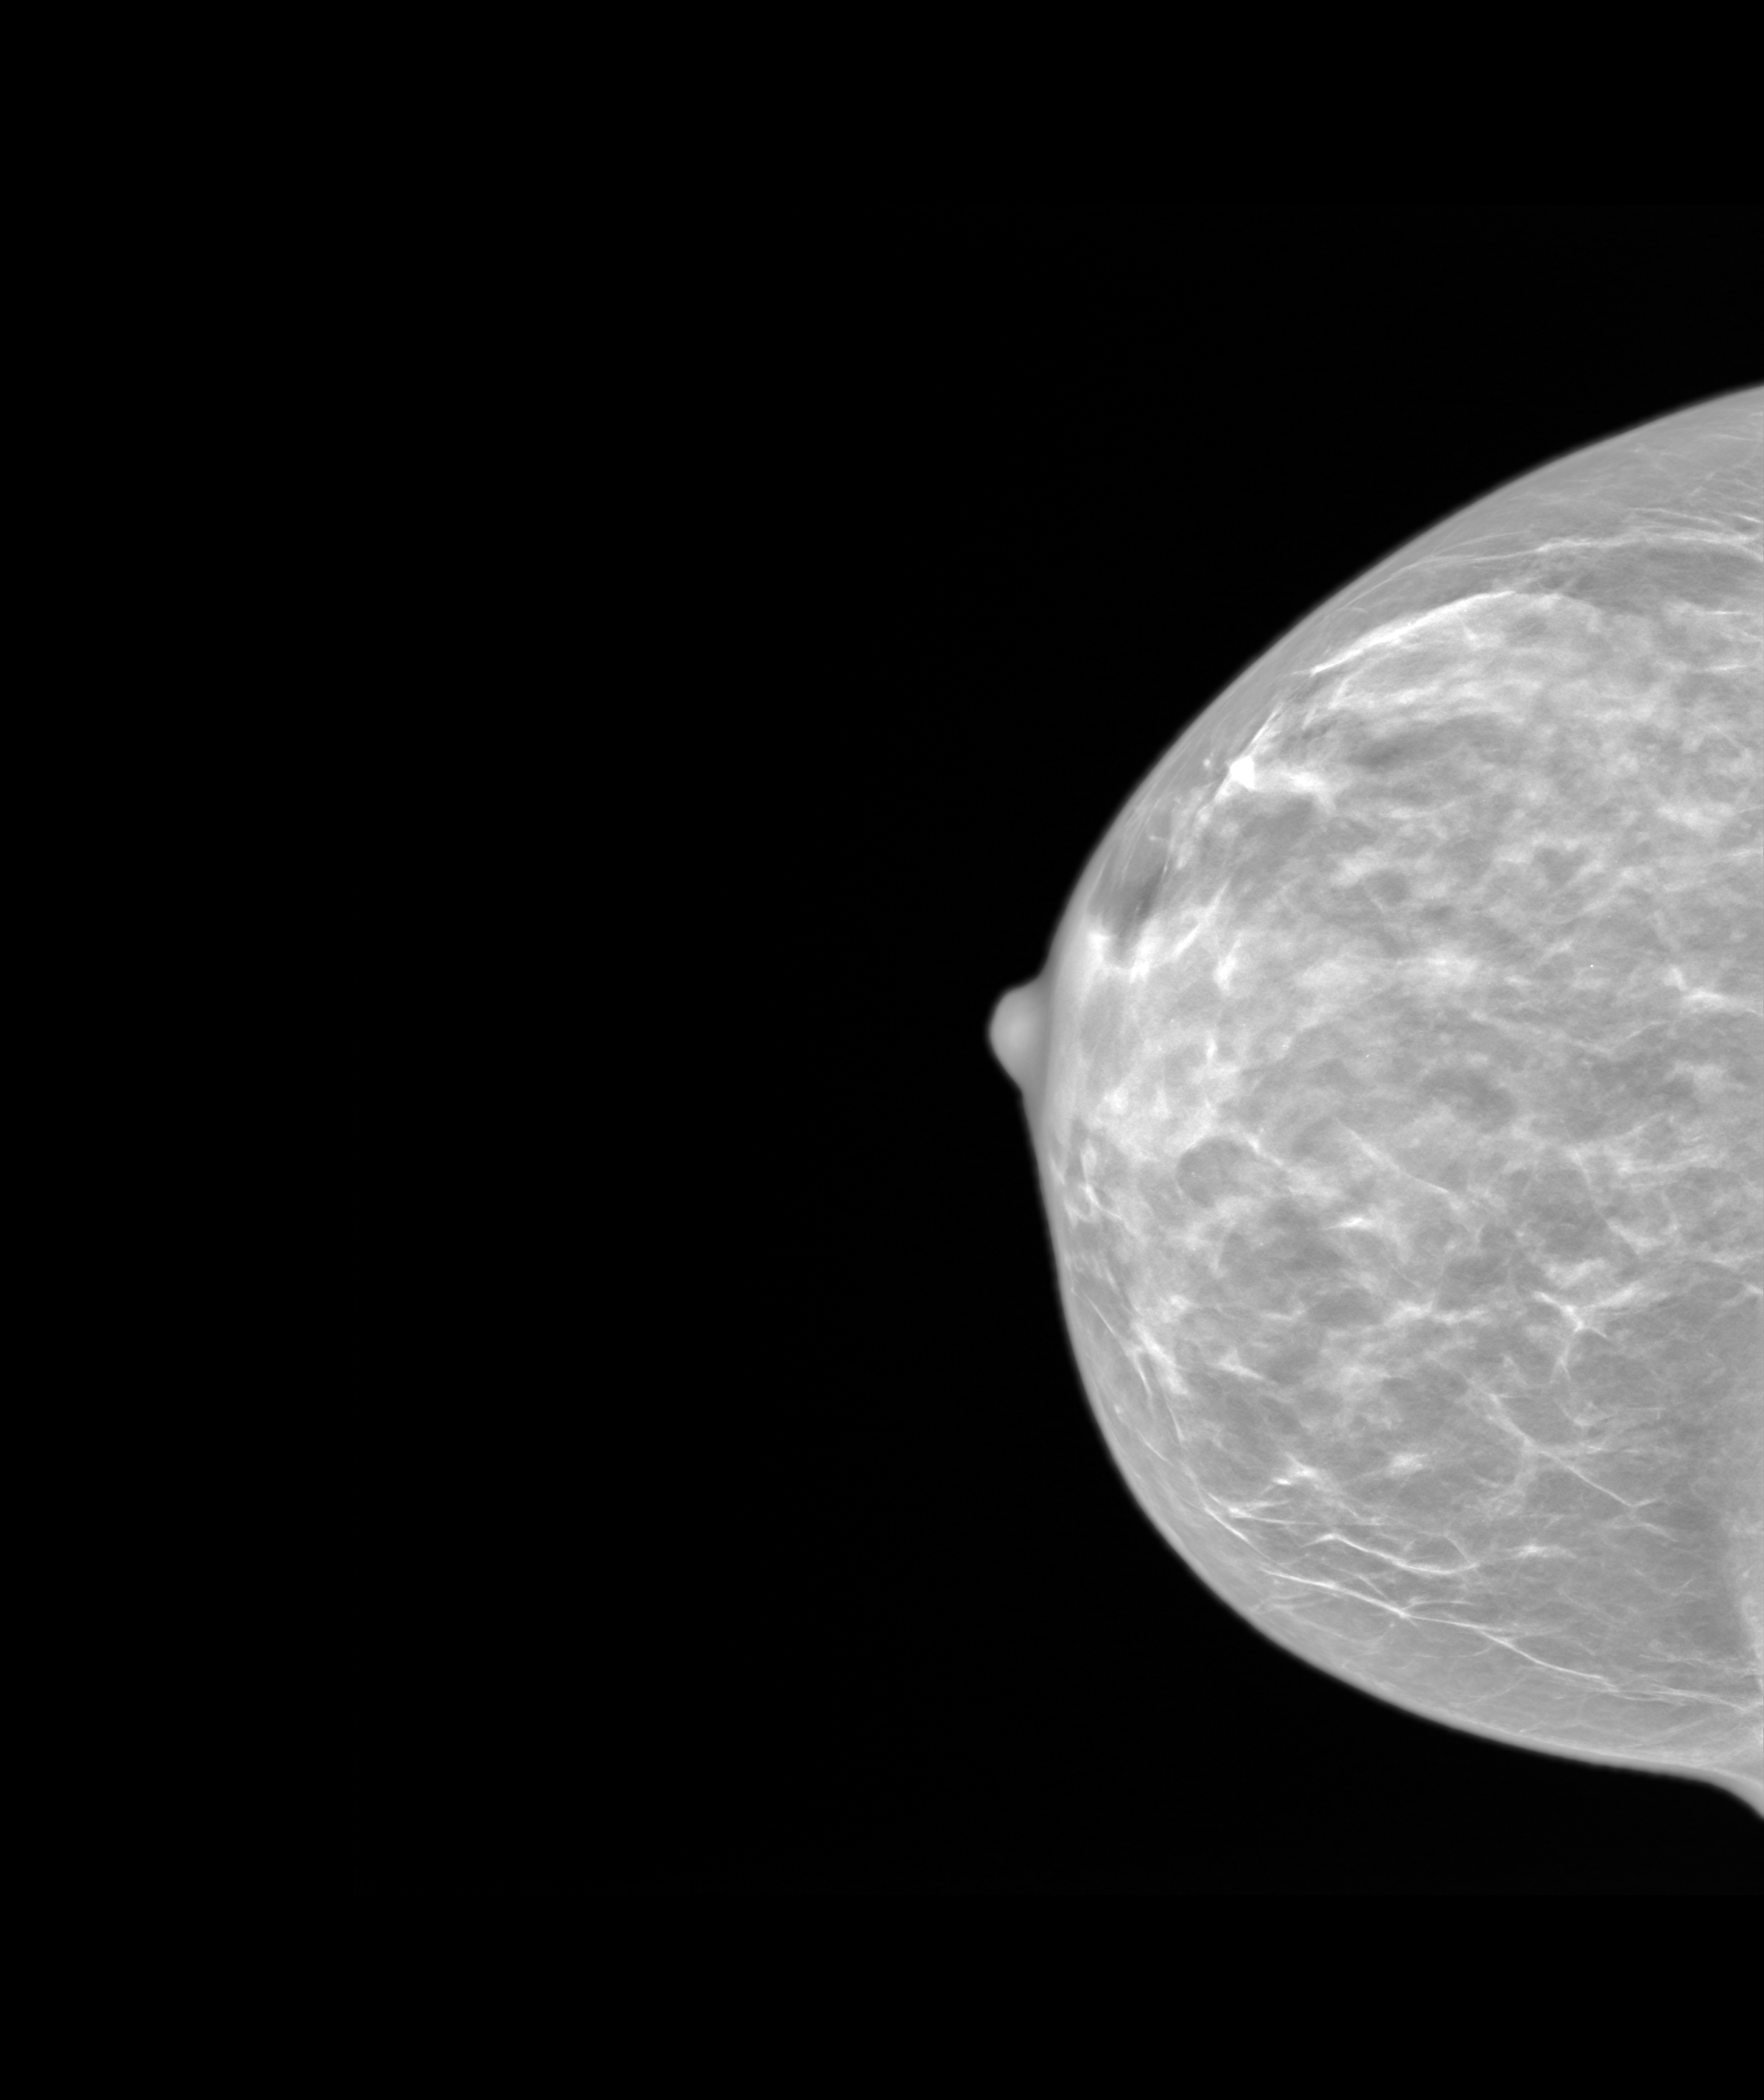
Screening examination. Female patient, age 48 years.
Image type: synthesized 2-D view from tomosynthesis. Breast: right. Projection: craniocaudal (CC) view.